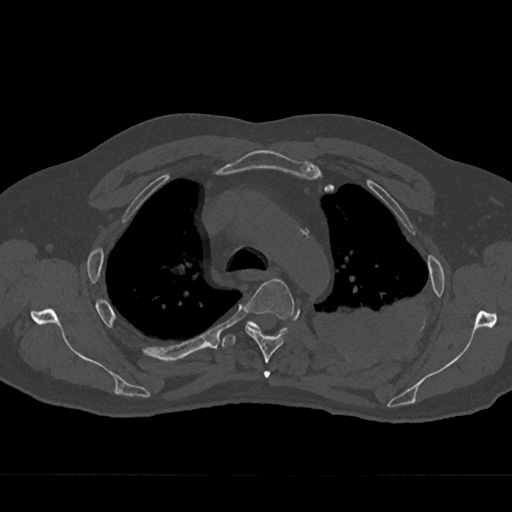
CT including the spine, one axial slice. Position 512 of 797 along the scan axis. 120 kVp. Bone window (W 1800 / L 400 HU). 0.5 mm slice thickness. 512 × 512 image matrix, field of view 377 × 377 mm. Male patient, age 75 years. From the clinical record (not read from this slice): primary cancer: renal.
Outlined on this slice (semi-automatically segmented with operator editing):
- T3 vertebra: bounding box (x1, y1, x2, y2) in pixels: (264, 371, 270, 378)
- T4 vertebra: (245, 279, 294, 363)
- T5 vertebra: (221, 321, 286, 348)